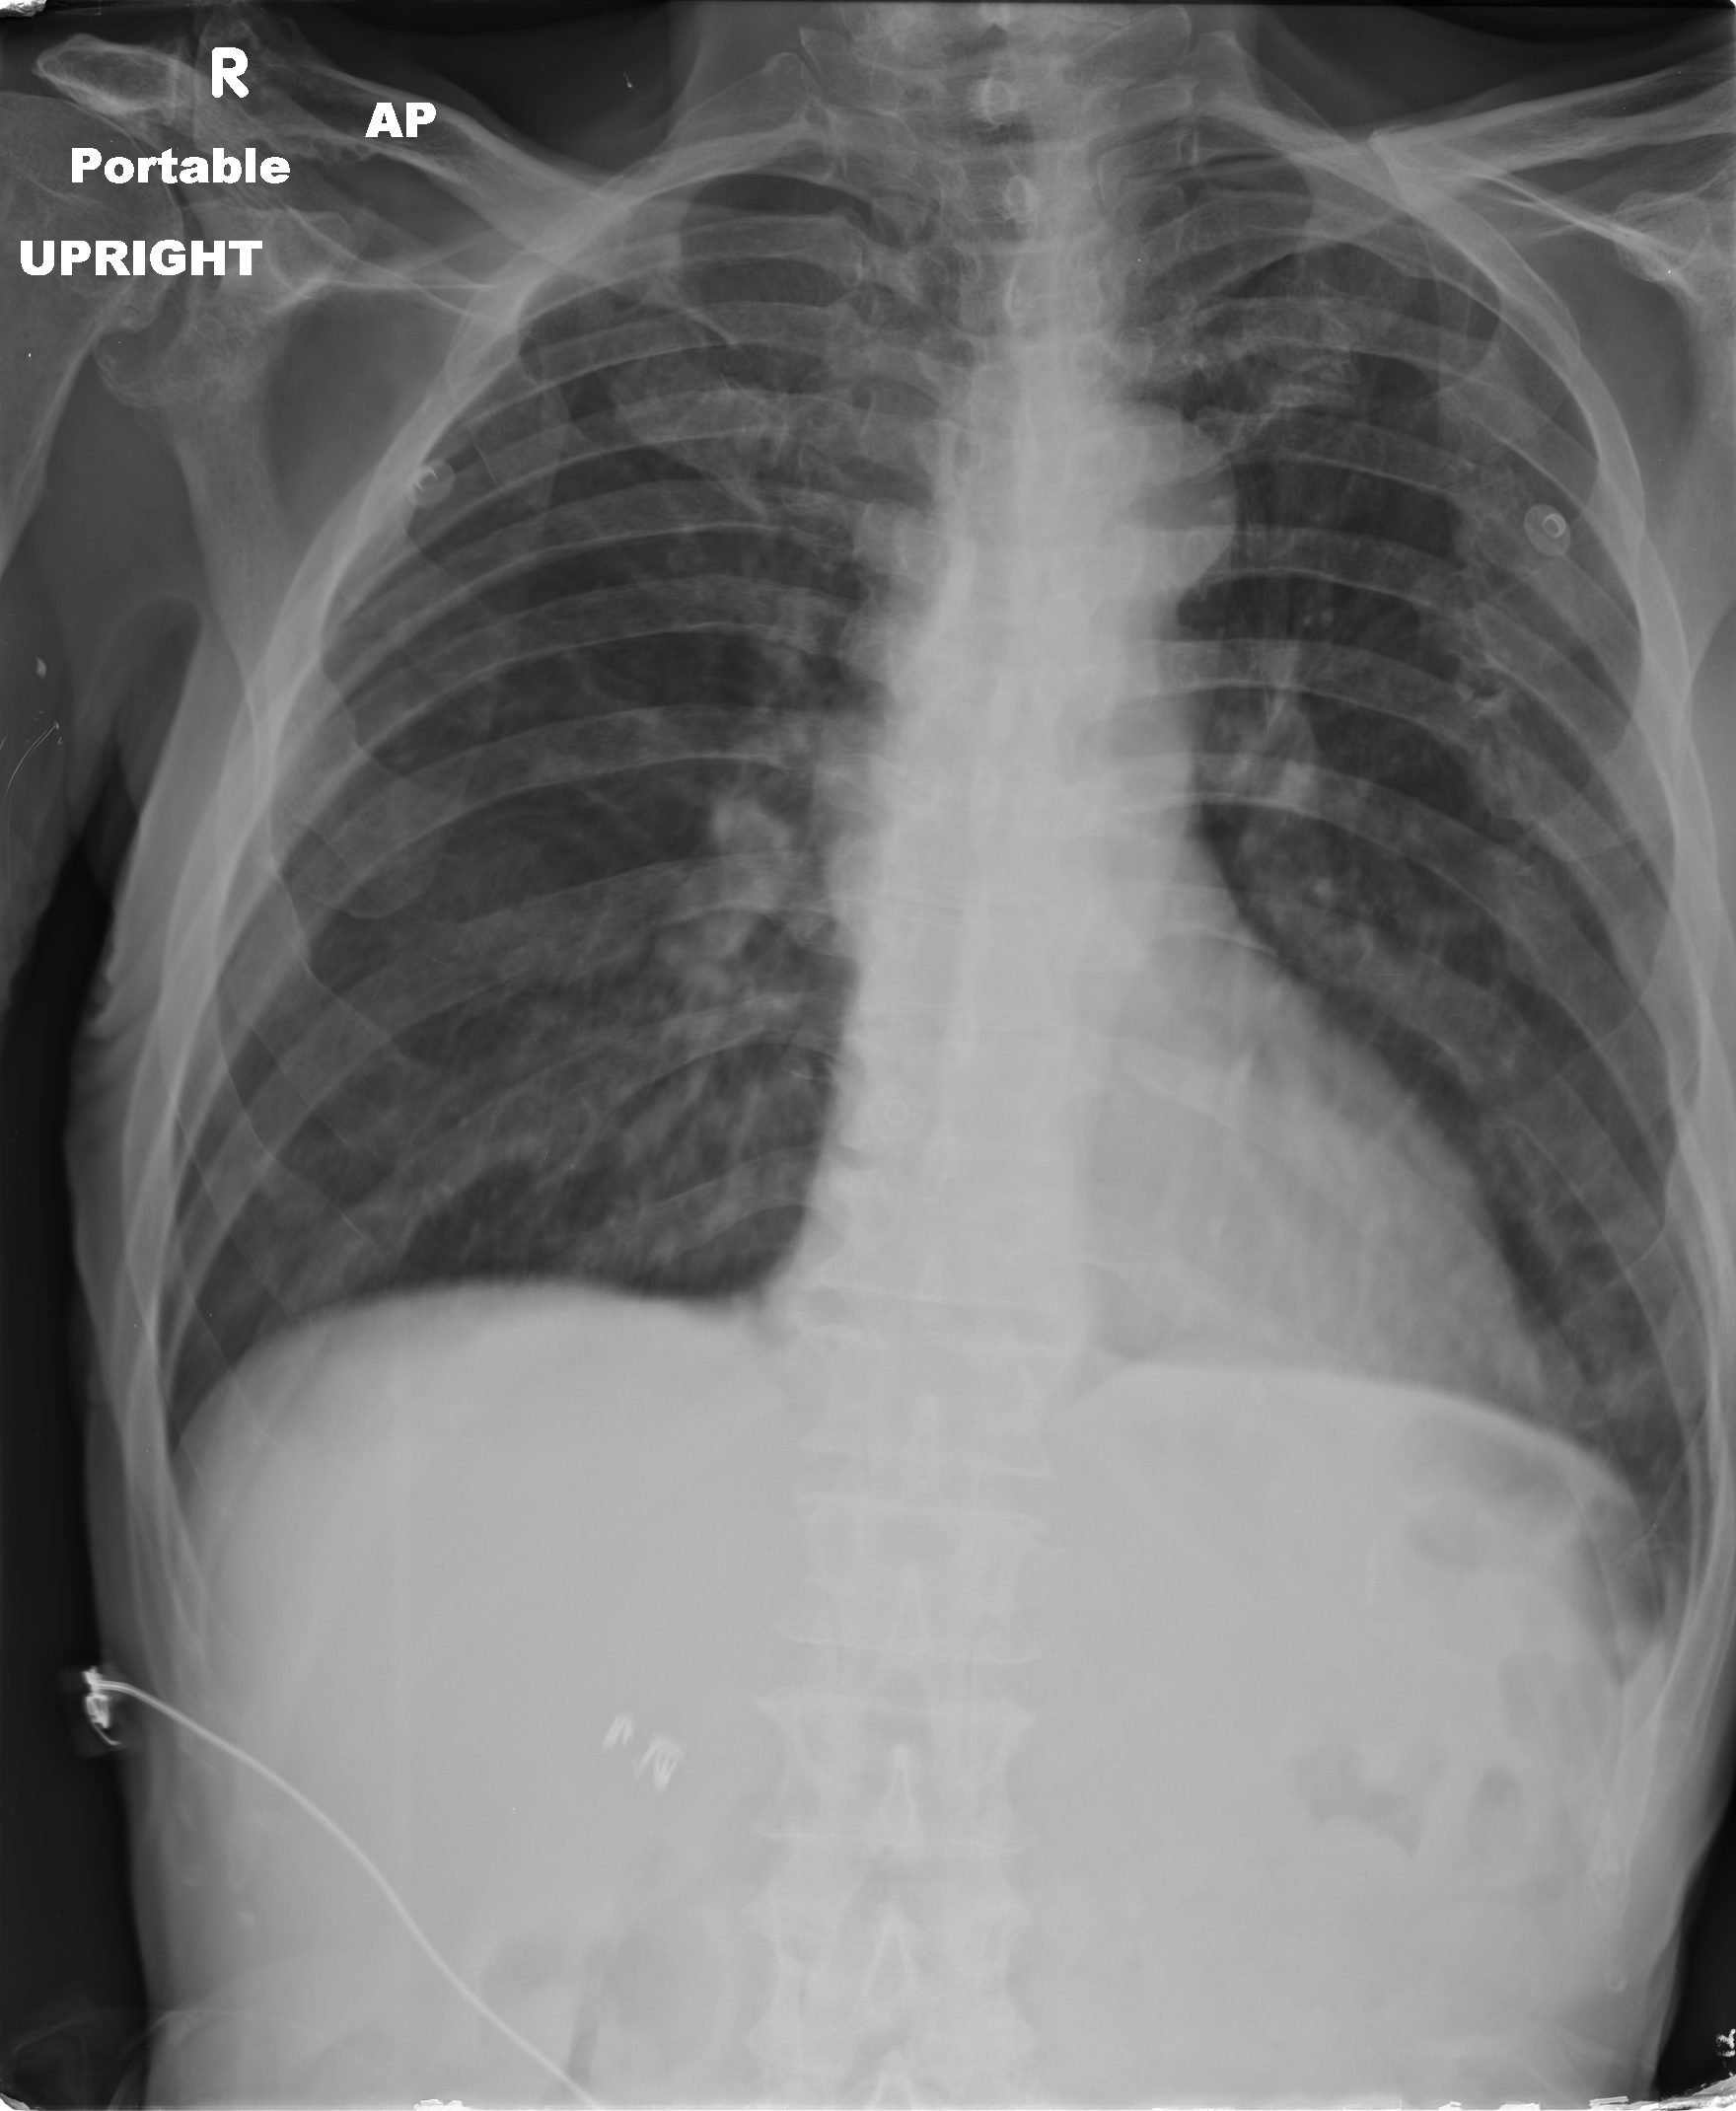
Chest X-ray, AP projection. Male patient, age 67 years; imaged 0 days after the COVID-19 diagnosis.
Radiologist's key findings for this exam: perinflated lungs with flattened diaphragms, suggestive of COPD.